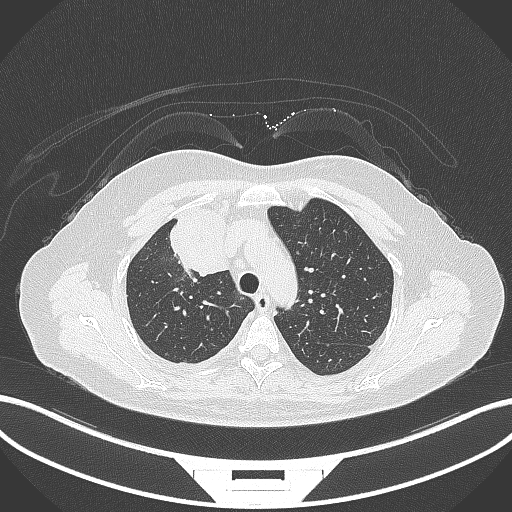
Chest CT, one axial slice; reconstruction kernel B70f; lung window (W 1500 / L -600 HU); 1 mm slice thickness; 512 × 512 image matrix. Patient: female, 52 years. Case-level facts recorded for this patient, not image findings: clinical TNM (as recorded): T3 N1 M1.
Outlined on this slice (rectangle marked by the reading radiologist):
- lung tumour (recorded histology: adenocarcinoma): bounding box (x1, y1, x2, y2) in pixels: (165, 205, 231, 278)